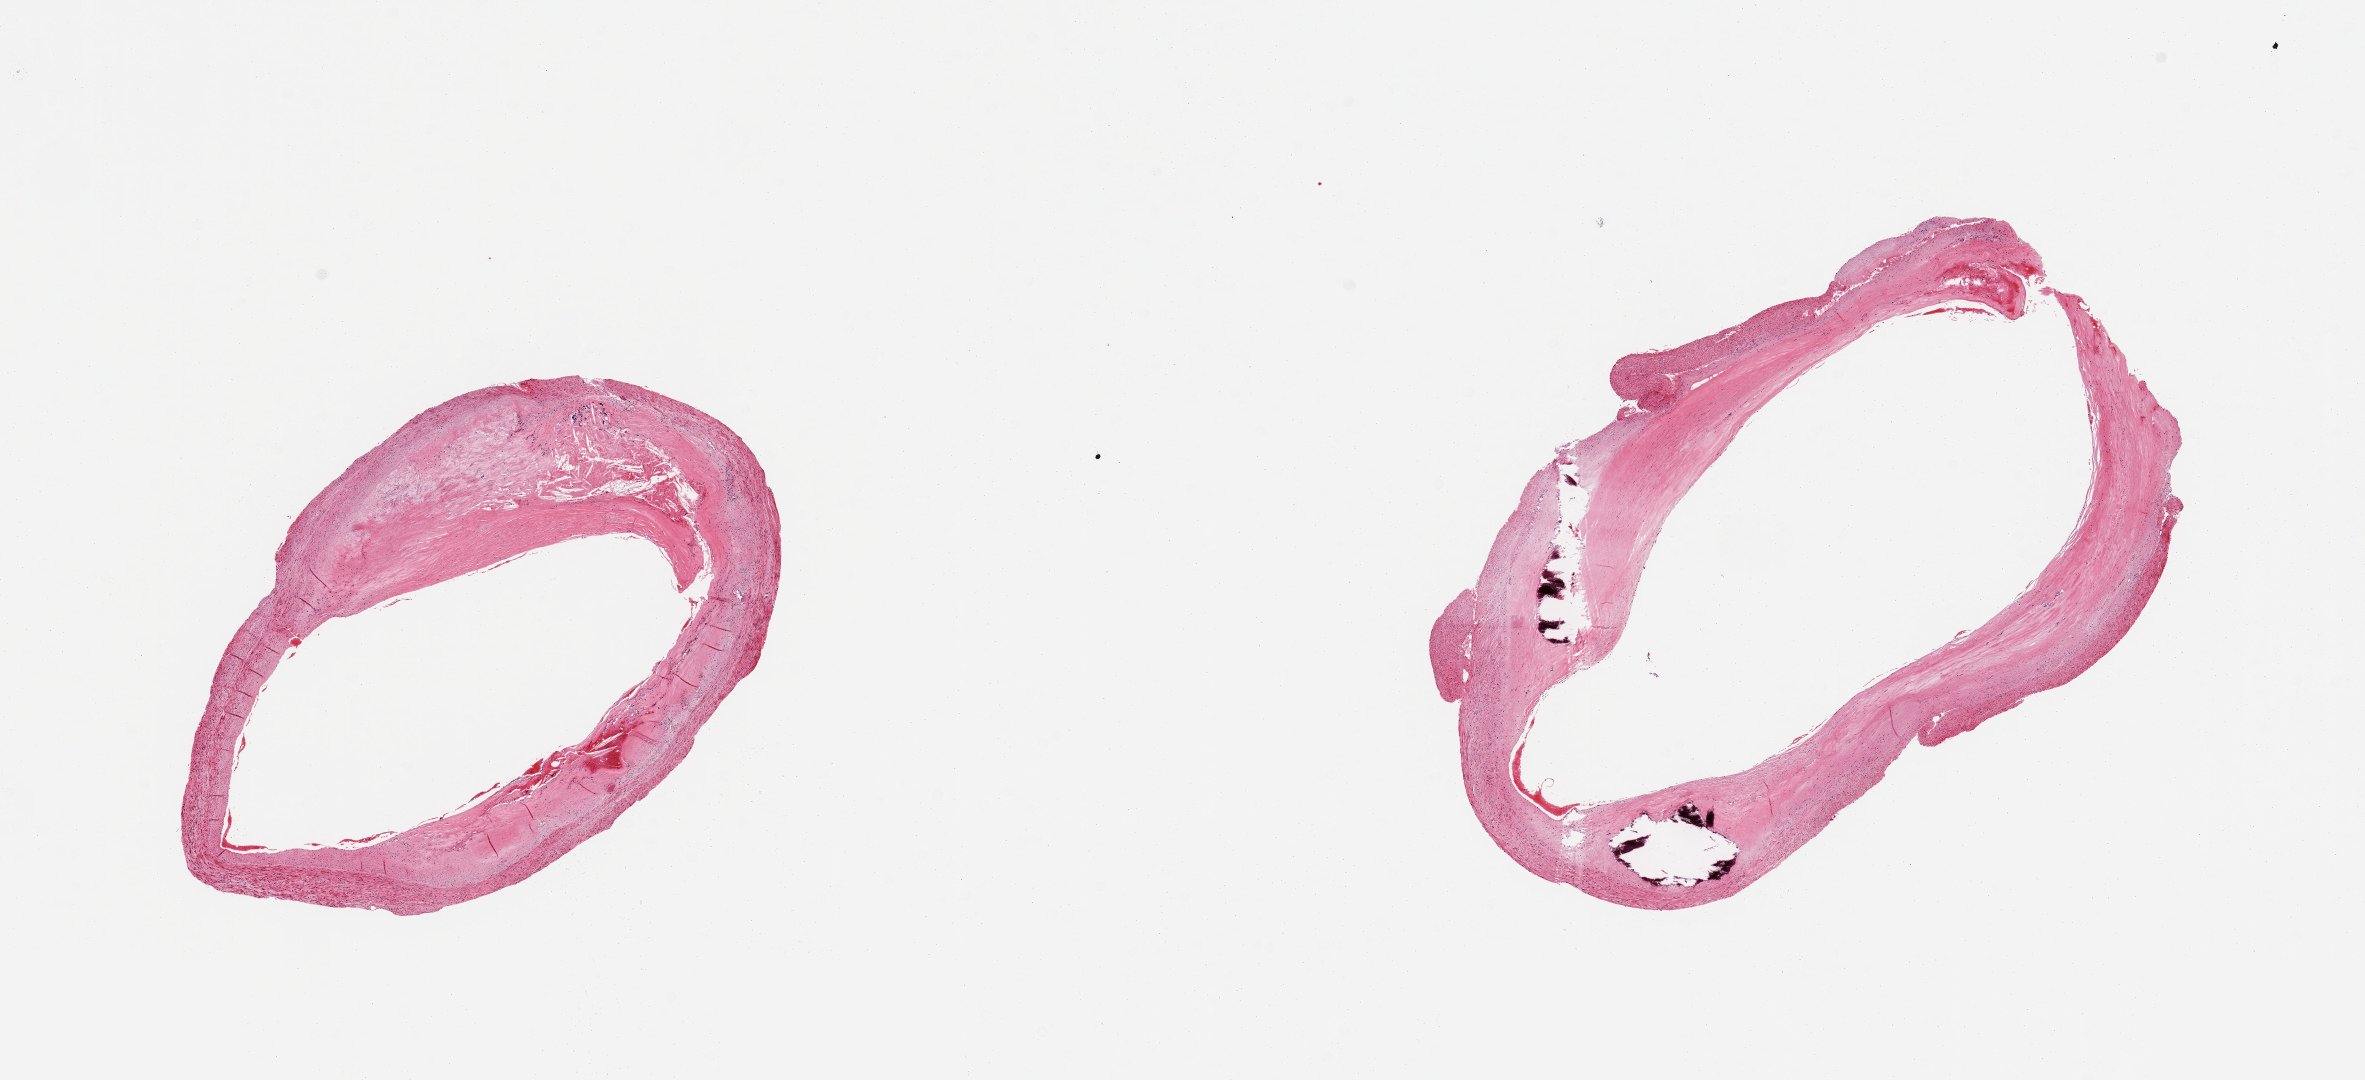
Whole-slide image, haematoxylin and eosin stain, brightfield — a low-resolution overview of the entire scanned area, about 18.7 x 8.5 mm (acquisition: 20x scan). PAXgene-fixed paraffin-embedded (PFPE) section. Target tissue: coronary artery. Donor tissue sample.
Reviewer comment on this tissue sample: 2 pieces, up to ~50% occlusive atherosis, focally calcified.